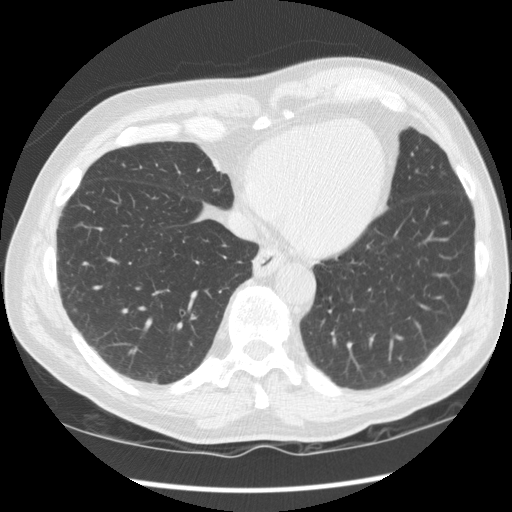
Chest CT (low-dose screening protocol), one axial image. Baseline screening round. Lung window (W 1500 / L -600 HU). 2.5 mm slice thickness. 512 × 512 image matrix. Male, age 71 years at enrolment.
Lesion marked by an expert reader, bounding box (x1, y1, x2, y2) in pixels: (132, 365, 173, 399). Reader record for this screening exam (exam-level; its link to the box is not recorded): non-calcified nodule or mass ≥4 mm, right upper lobe, 26 × 15 mm, smooth margins, mixed attenuation. Official screen result: positive, change unspecified: nodule(s) >= 4 mm or enlarging nodule(s), mass(es), or other non-specific abnormalities suspicious for lung cancer. Participant outcome: lung cancer diagnosed 357 days after this screen — squamous cell carcinoma, NOS, right lower lobe, moderately differentiated (G2), stage IA (AJCC 6th edition), 27 mm at pathology.